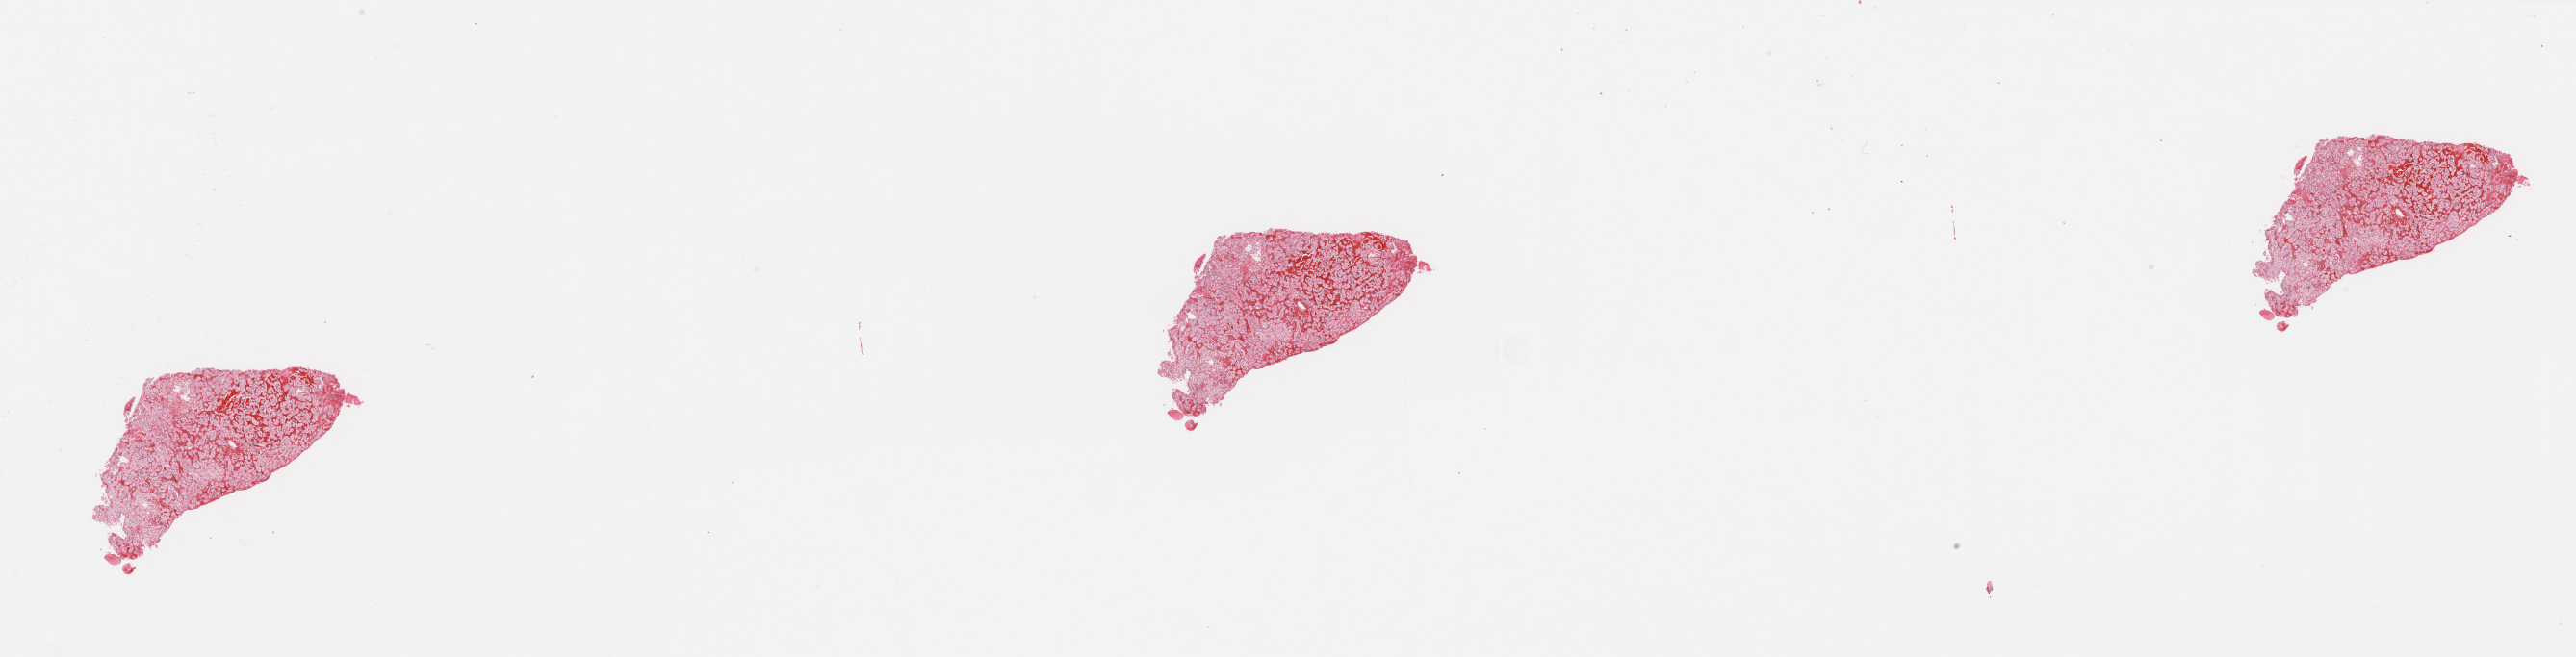
Digitized Hematoxylin and eosin (H&E) stained tissue section (whole slide) — shown as a low-resolution overview of the whole scanned area (about 42.3 x 10.8 mm, acquisition: 20x scan), tumour tissue sample, sampled site: kidney. Patient: male, age 47 years. Histologic grade: G2 (moderately differentiated). Pathologist review of this section (percent, as recorded): tumour nuclei 80%, necrosis 10%.
Primary tumour site (as recorded): upper pole. AJCC pathologic stage: I. Histologic diagnosis: Renal cell carcinoma, NOS.